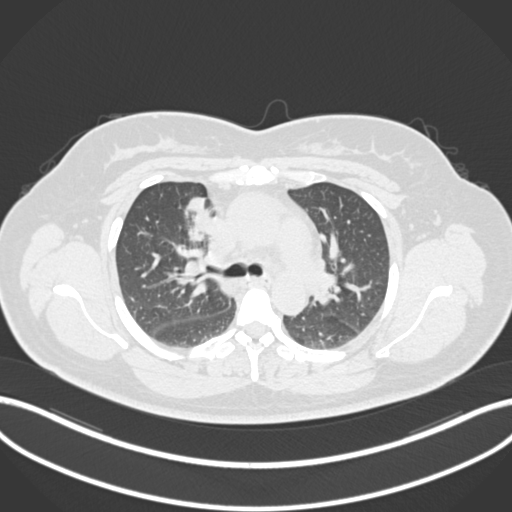
Chest CT, one axial slice; position 119 of 183 along the scan axis; lung window (W 1500 / L -600 HU); 512 × 512 image matrix. Patient: female, 46 years. Case-level facts recorded for this patient, not image findings: clinical TNM (as recorded): T2a N1 M0.
Annotated regions visible in this slice (rectangle marked by the reading radiologist):
- lung tumour (recorded histology: adenocarcinoma): box from (x=182, y=192) to (x=213, y=237) px